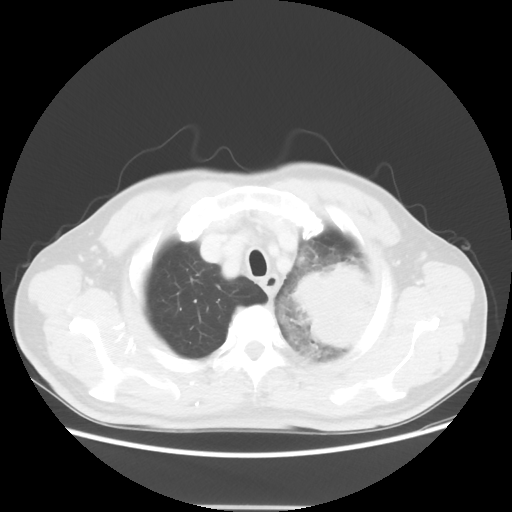
Chest CT, one axial slice; position 48 of 53 along the scan axis; reconstruction kernel STANDARD; lung window (W 1500 / L -600 HU); 512 × 512 image matrix. Patient: male, 60 years. From the clinical record (not read from this slice): clinical TNM (as recorded): T4 N1 M1a; histopathological grade: G3.
Structures marked on this image (rectangle marked by the reading radiologist):
- lung tumour (recorded histology: large cell carcinoma): box from (x=284, y=250) to (x=388, y=356) px